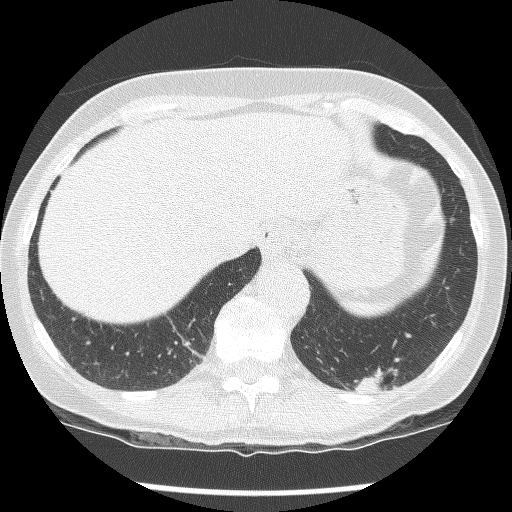
Axial slice from a low-dose chest CT screening exam. Second annual screen. Lung window (W 1500 / L -600 HU). Slice 106 of 136 in the series. 512 × 512 image matrix. Female participant, aged 61 years at enrolment. Current smoker at enrolment.
Expert-annotated lung lesion, bounding box [x1, y1, x2, y2] px = [326, 308, 440, 412]. The screening reader recorded 2 non-calcified nodules or masses ≥4 mm on this exam (left lower lobe, left lower lobe); which of them this box marks is not recorded. Official screen result: positive, no significant change: stable abnormalities potentially related to lung cancer, unchanged since the prior screening exam. Participant outcome: lung cancer diagnosed 585 days after this screen (after the third annual screen) — non-small cell carcinoma, left lower lobe, poorly differentiated (G3), stage IB (AJCC 6th edition), 100 mm at pathology.